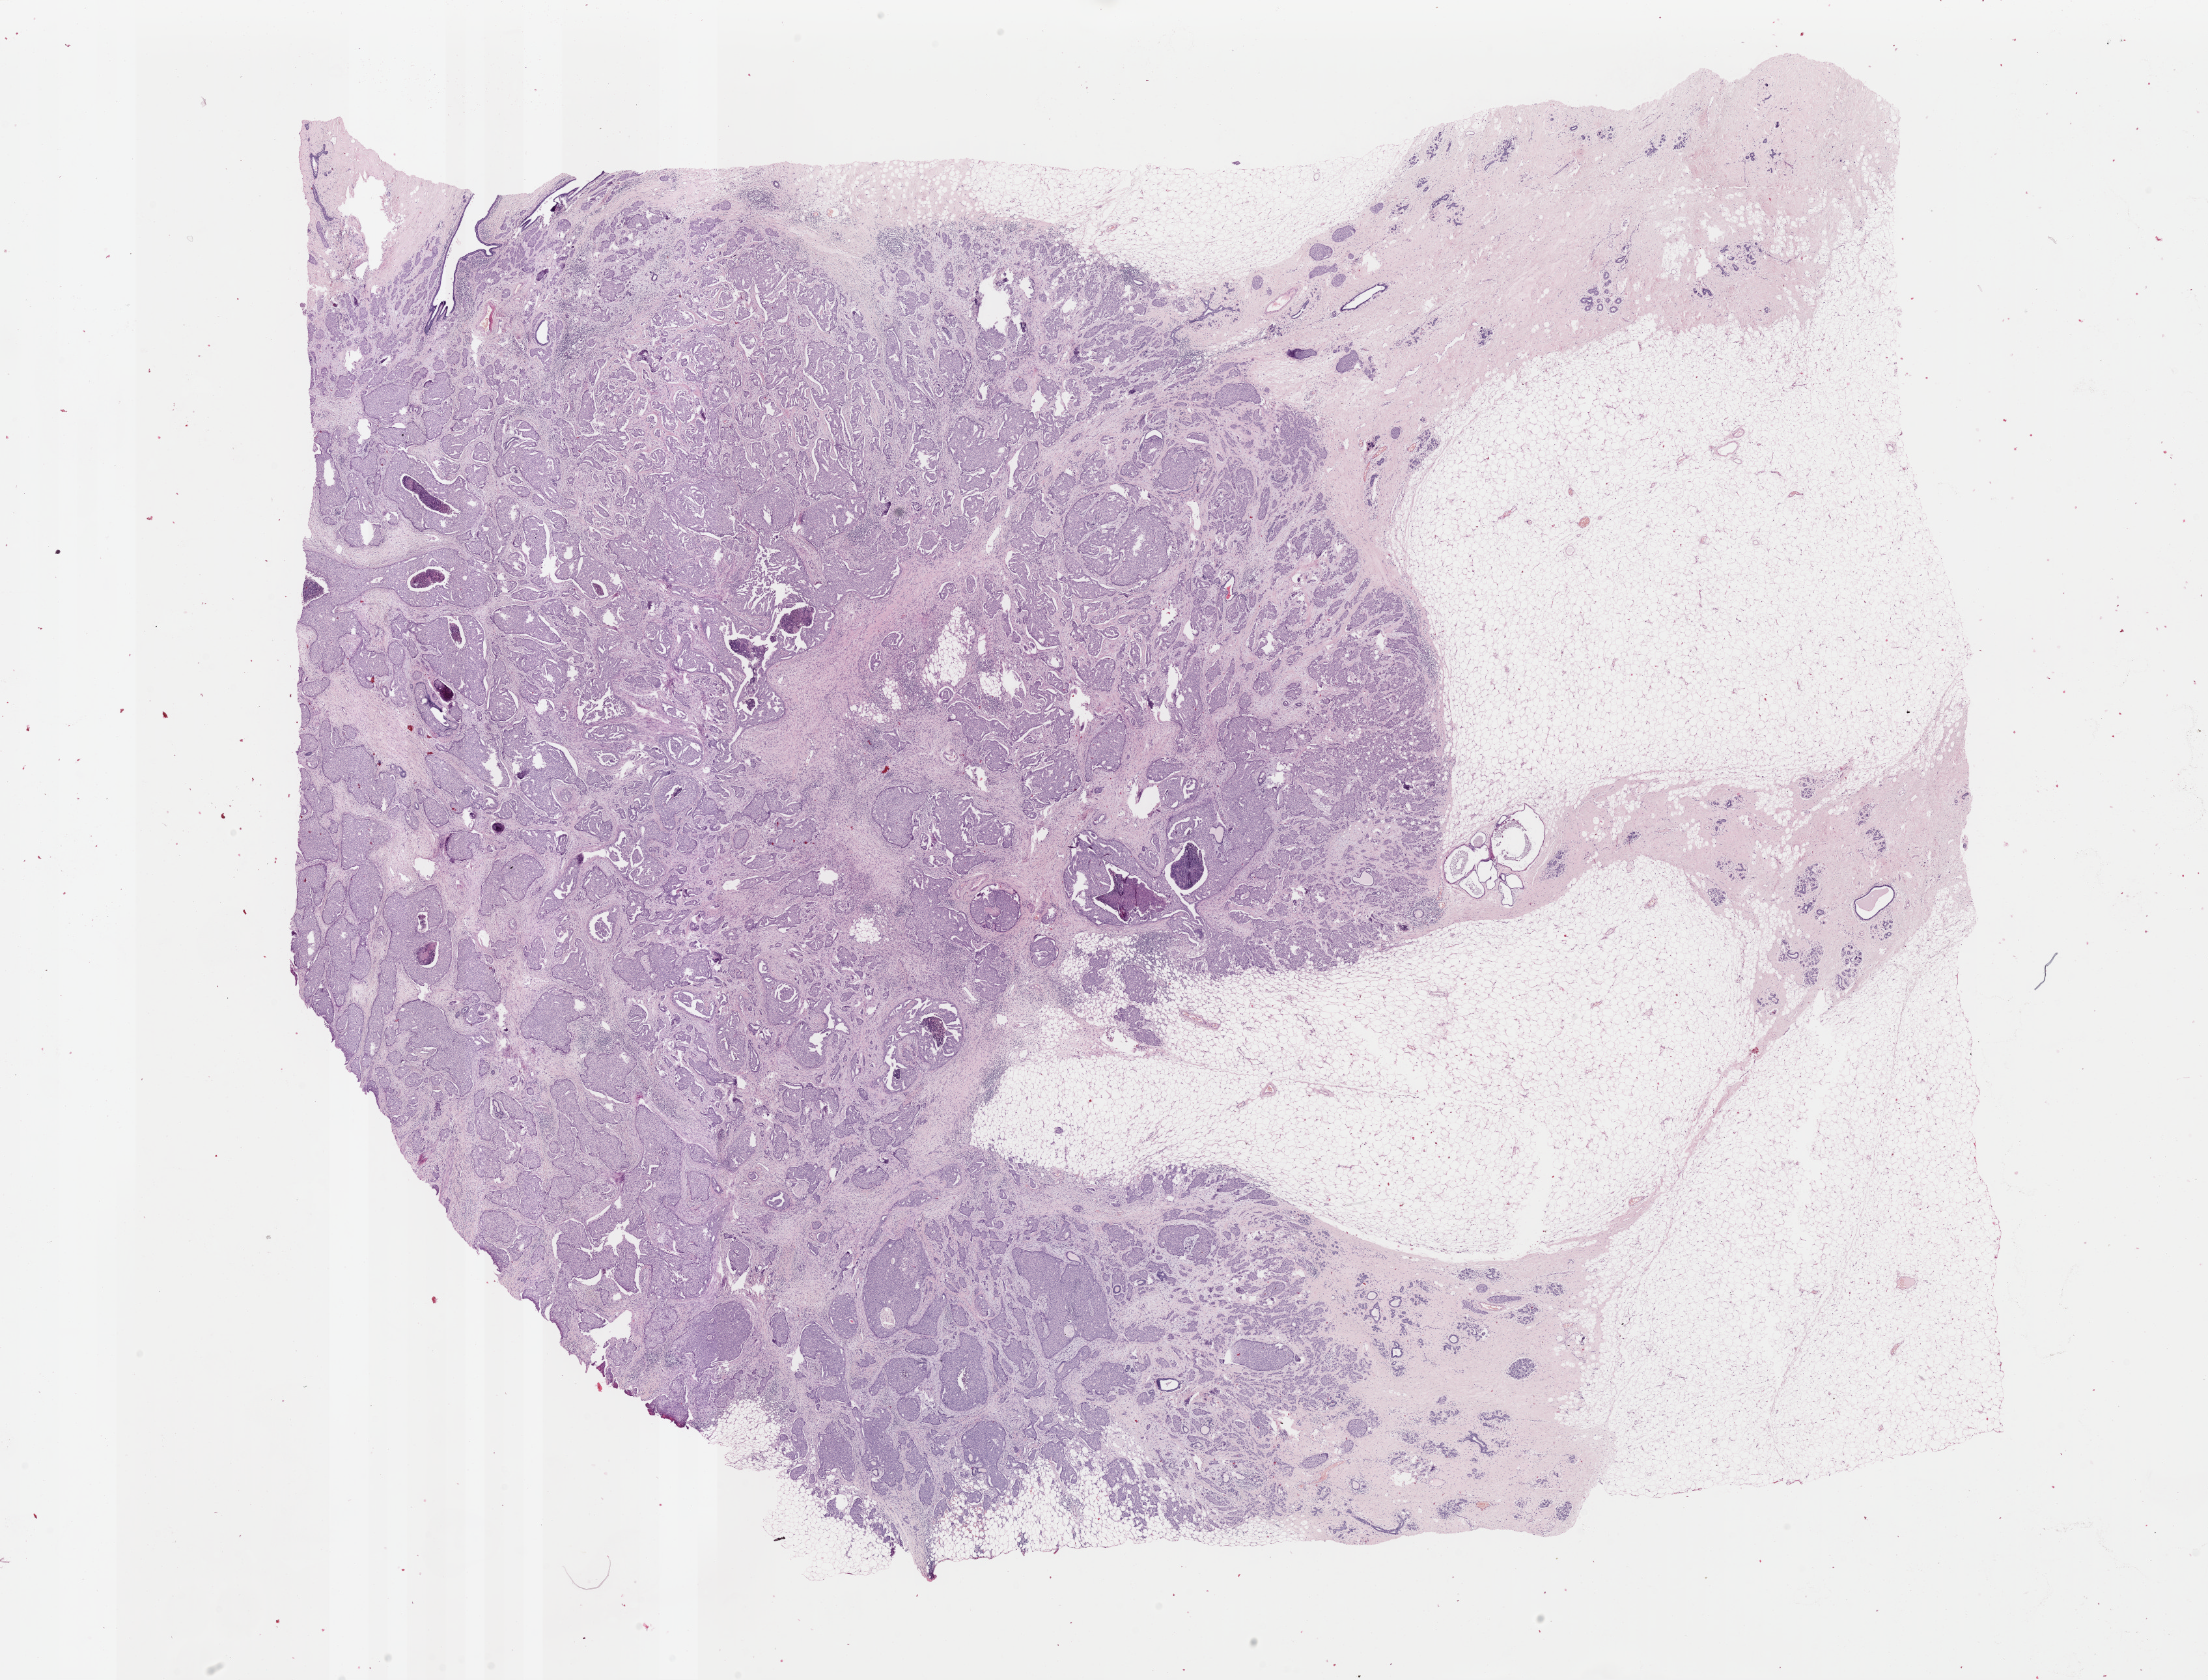
Digitized Hematoxylin and eosin (H&E) stained tissue section (whole slide) — shown as a low-resolution overview of the whole scanned area (about 26.8 x 20.4 mm); formalin-fixed paraffin-embedded (FFPE) diagnostic section; primary tumour sample from the breast. Female patient; age at initial diagnosis 36 years.
• lymph nodes positive (case pathology): 6 of 18 examined
• diagnosis: Infiltrating duct carcinoma, NOS
• TNM: T1c N2a M0
• AJCC pathologic stage: IIIA (7th edition)